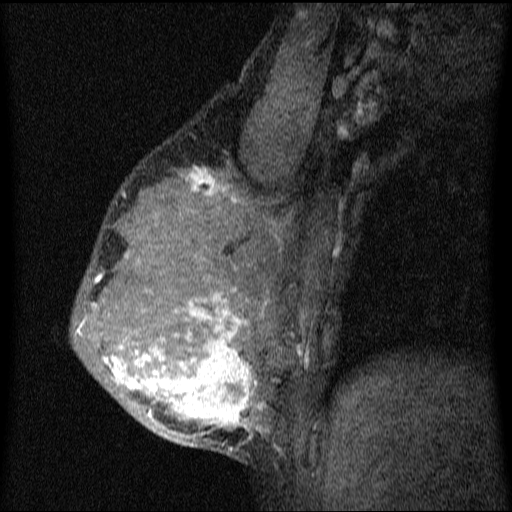
Breast MRI (dynamic contrast-enhanced), one sagittal slice. Position 44 of 64 along the scan axis. Dynamic contrast-enhanced series, image 2 of 4 at this slice position (ordered by acquisition). 1.5 T. TE 4.2 ms, TR 9.1 ms. 2 mm slice thickness. 512 × 512 image matrix, field of view 180 × 180 mm. Patient: female, 33 years.
Structures marked on this image (semi-automatically segmented with operator editing):
- analysis volume of interest (the breast-tissue region the enhancement analysis was run in; not a lesion): bounding box (x1, y1, x2, y2) in pixels: (71, 151, 336, 458)
- tumour enhancement mask (voxels above the 70 % enhancement threshold inside the analysis volume of interest): (76, 168, 309, 444)